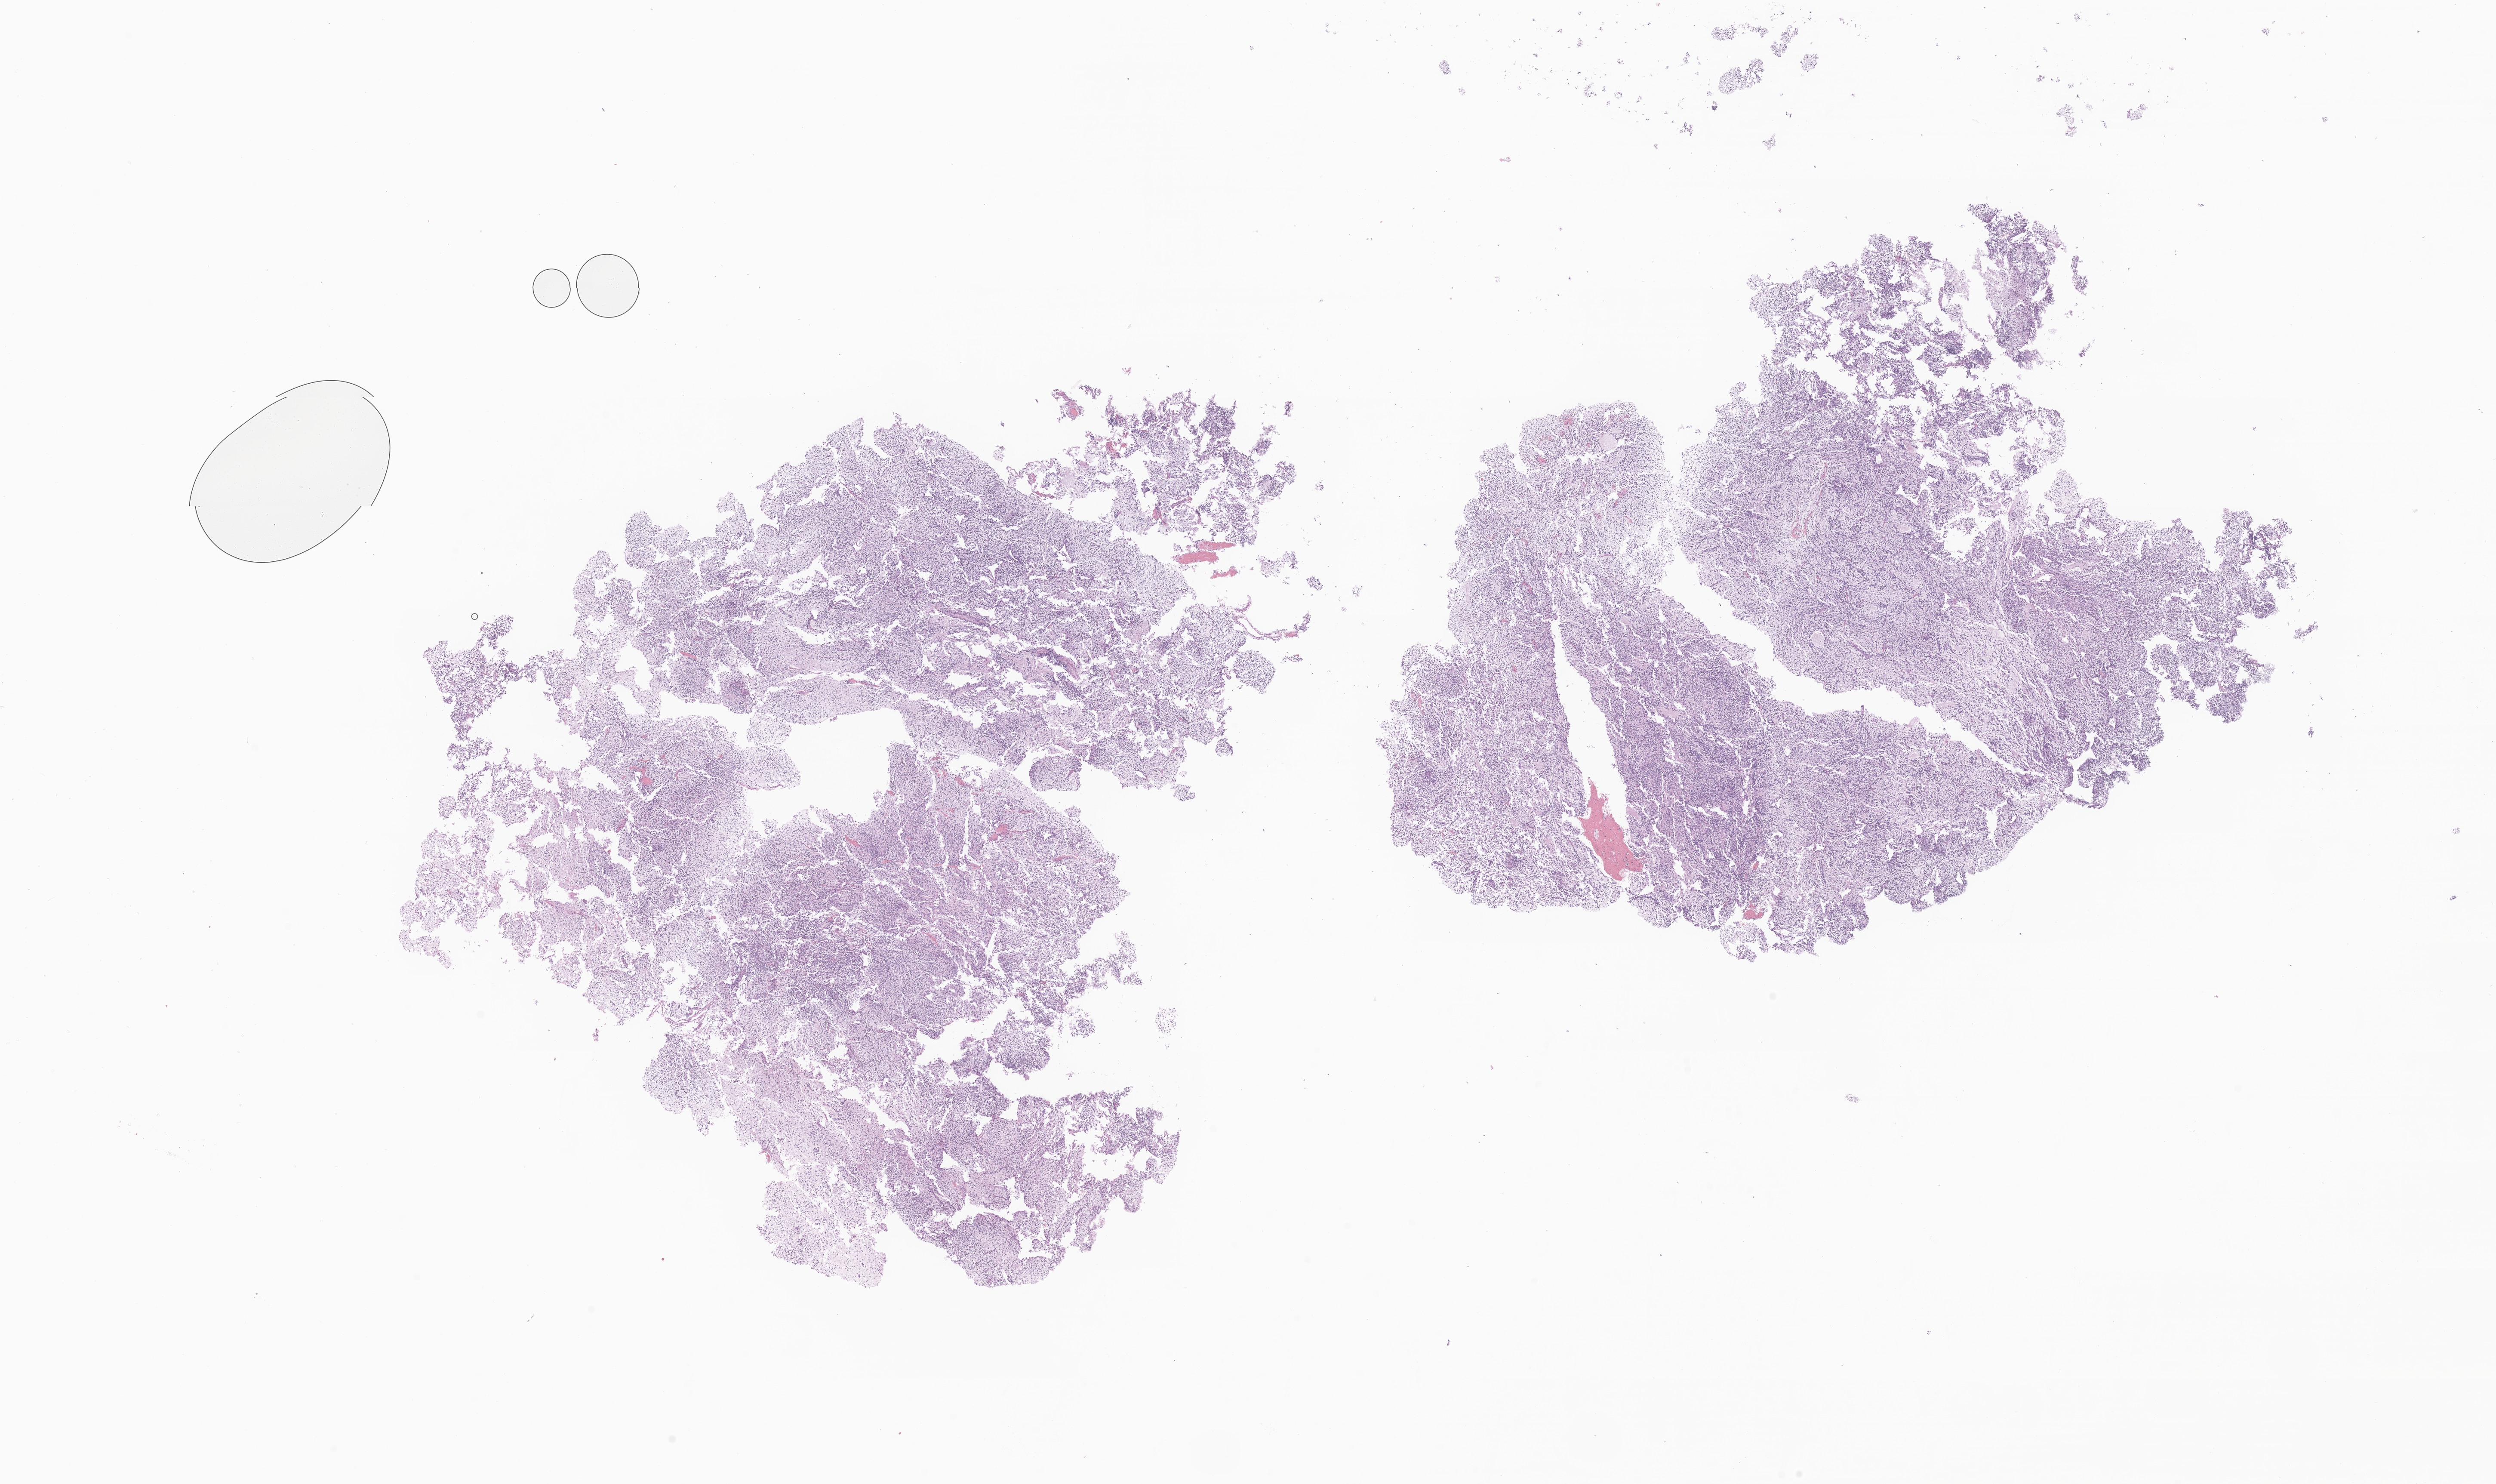
H&E whole-slide image of tumor tissue from the frontal lobe, low-resolution overview of the scanned area, about 24.5 x 14.5 mm; formalin-fixed, paraffin-embedded (FFPE) tissue. Patient: male, age 49 months (4 years 1 month).
Recorded diagnosis: Neoplasm, malignant.